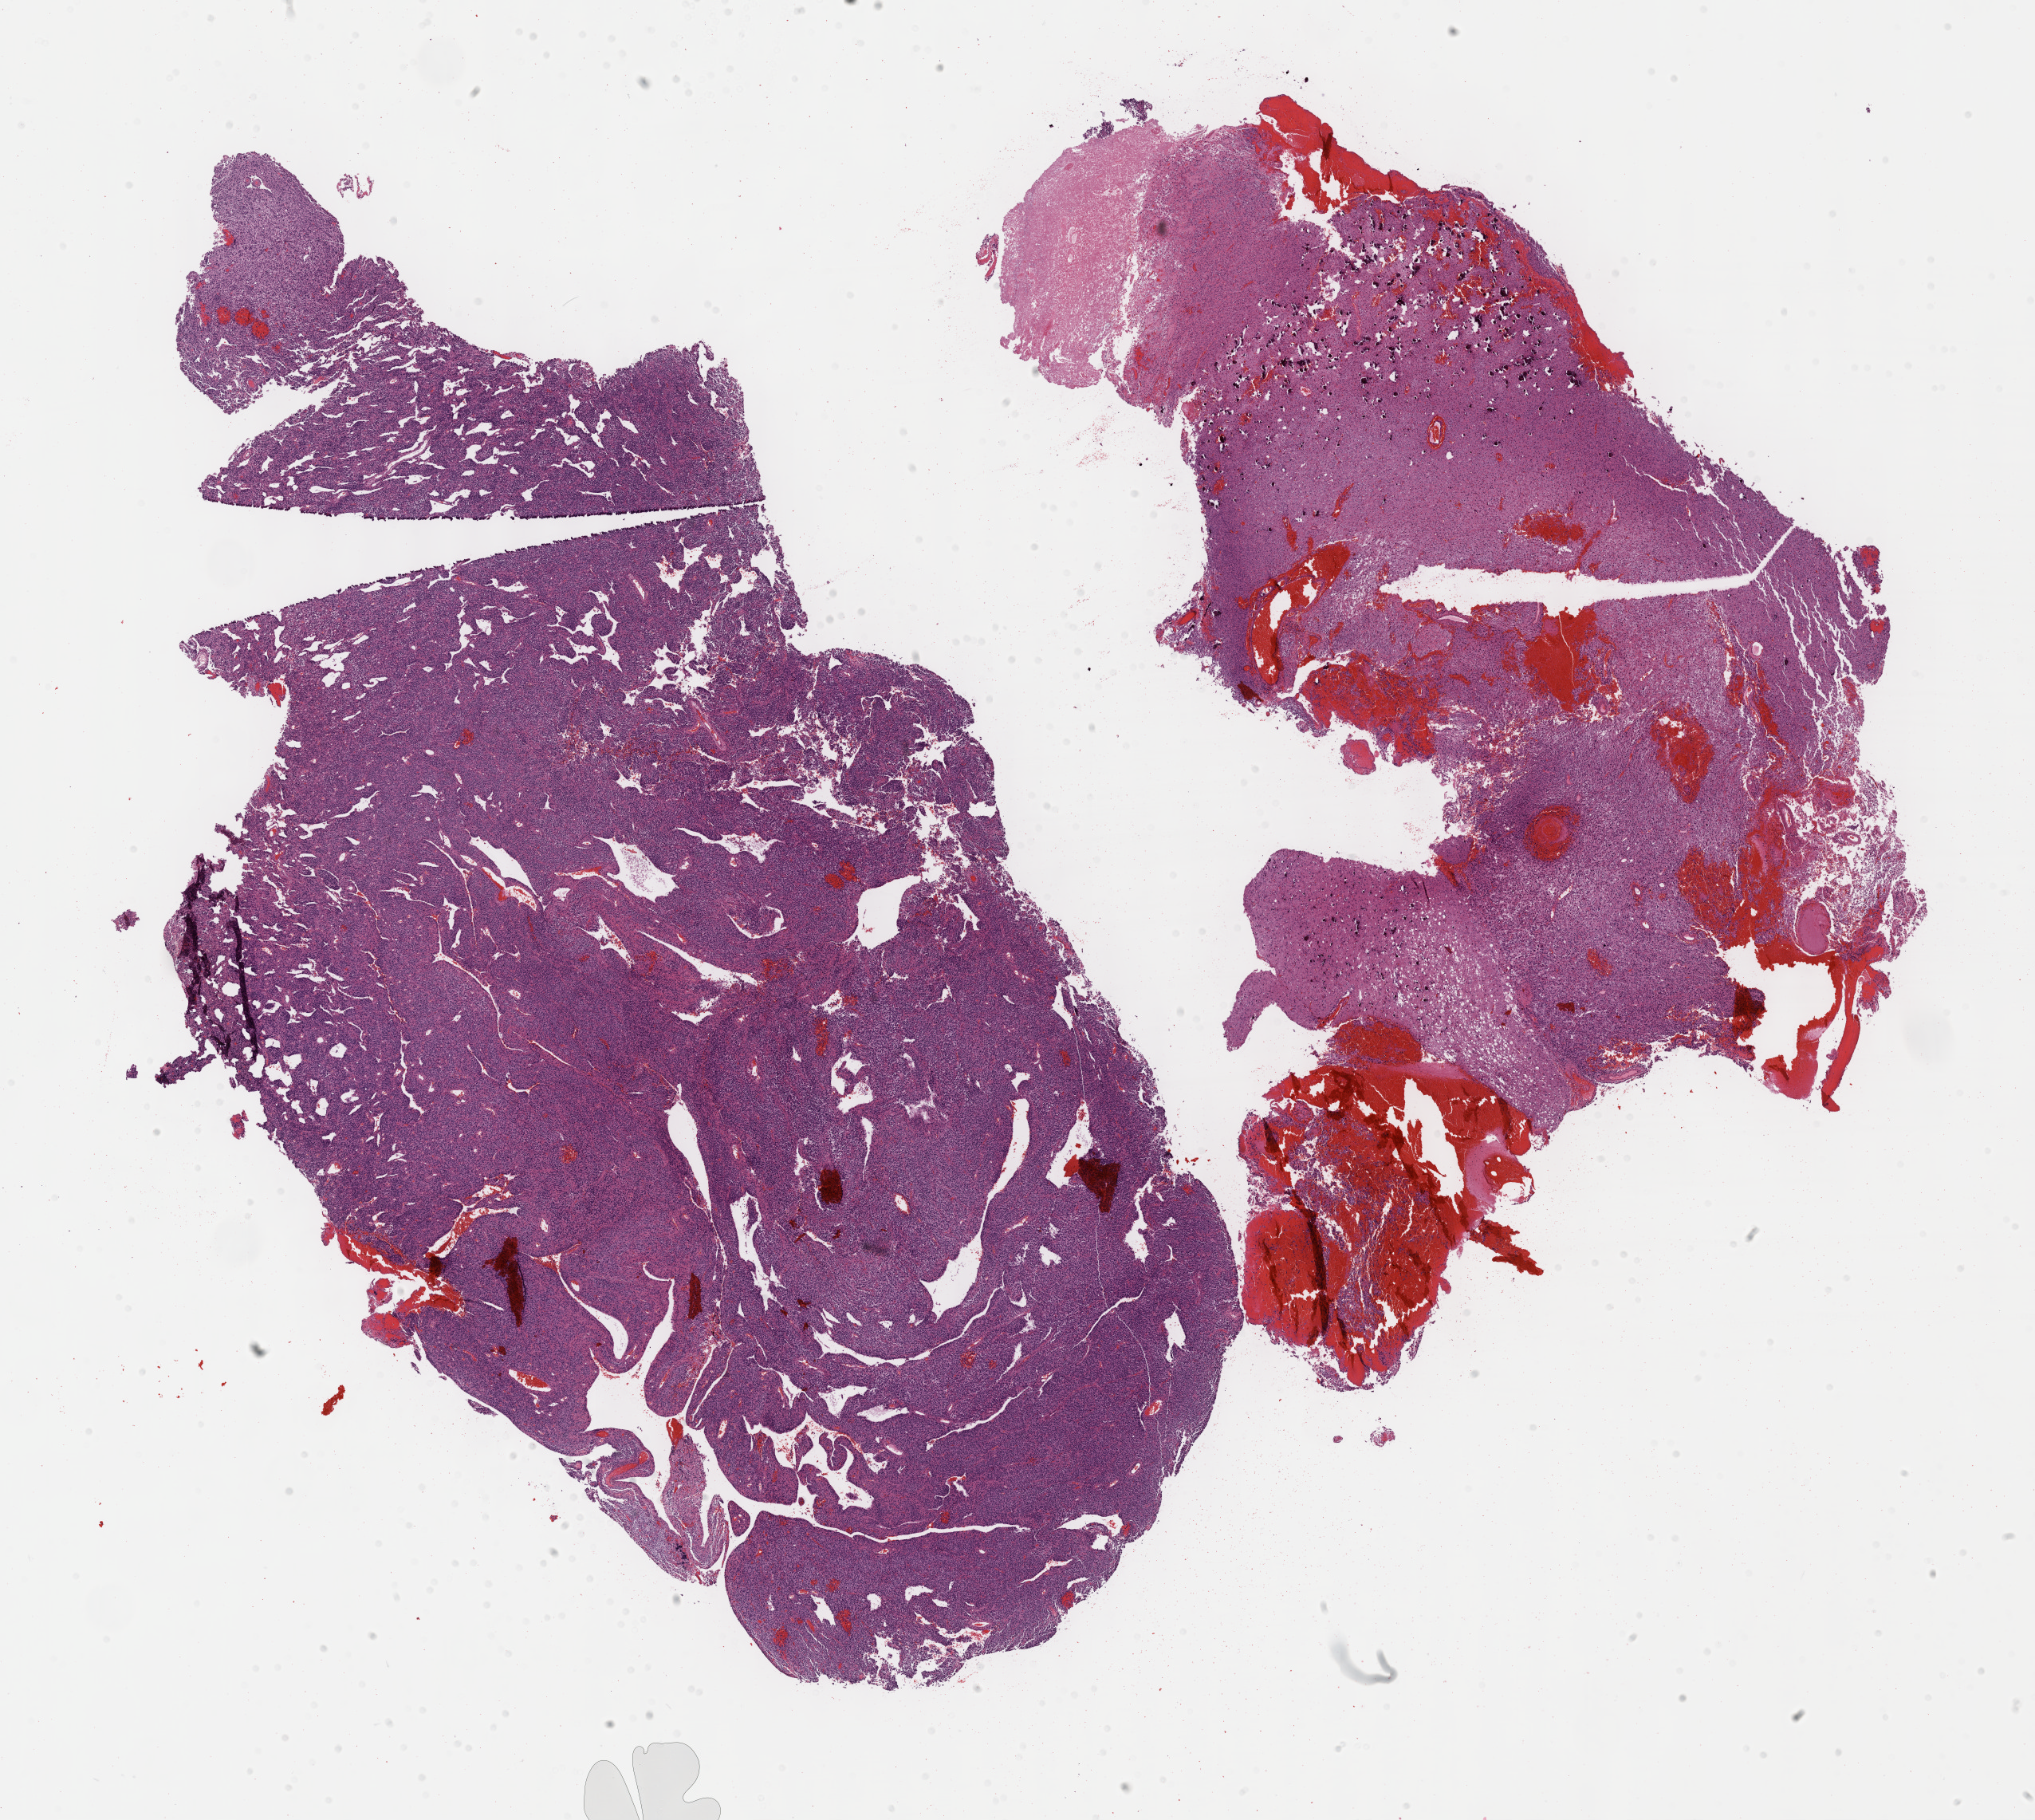
Whole-slide histology image, Hematoxylin and eosin (H&E) stained — whole scanned area (about 20.6 x 18.5 mm) shown as a low-resolution overview; formalin-fixed paraffin-embedded (FFPE) diagnostic section; brain, primary tumour sample. Male patient; age at initial diagnosis 29 years. Histologic grade: G3 (poorly differentiated).
Pathologic diagnosis: Mixed glioma.